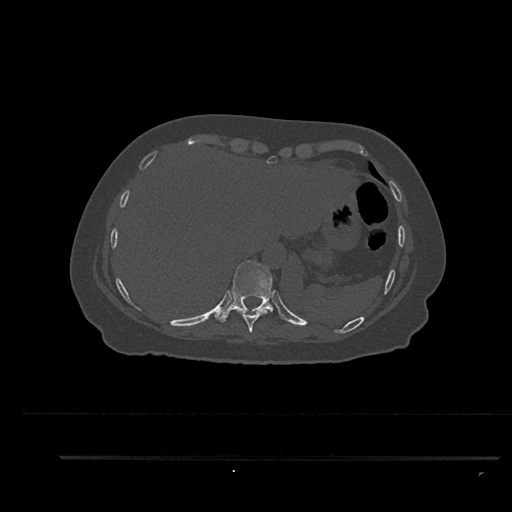
CT including the spine, one axial slice. Slice 388 of 797 in the series (ordered by position). Reconstruction kernel Br40s/3. 120 kVp. Bone window (W 1800 / L 400 HU). 0.5 mm slice thickness. 512 × 512 image matrix. Female patient, age 44 years. Case-level facts recorded for this patient, not image findings: primary cancer: renal; vertebrae with lytic lesions (as recorded): L1.
Structures marked on this image (semi-automatic segmentation, software-assisted and operator-edited):
- T10 vertebra: bounding box <216,260,280,323> (left, top, right, bottom; pixels)
- T9 vertebra: <237,309,267,338>